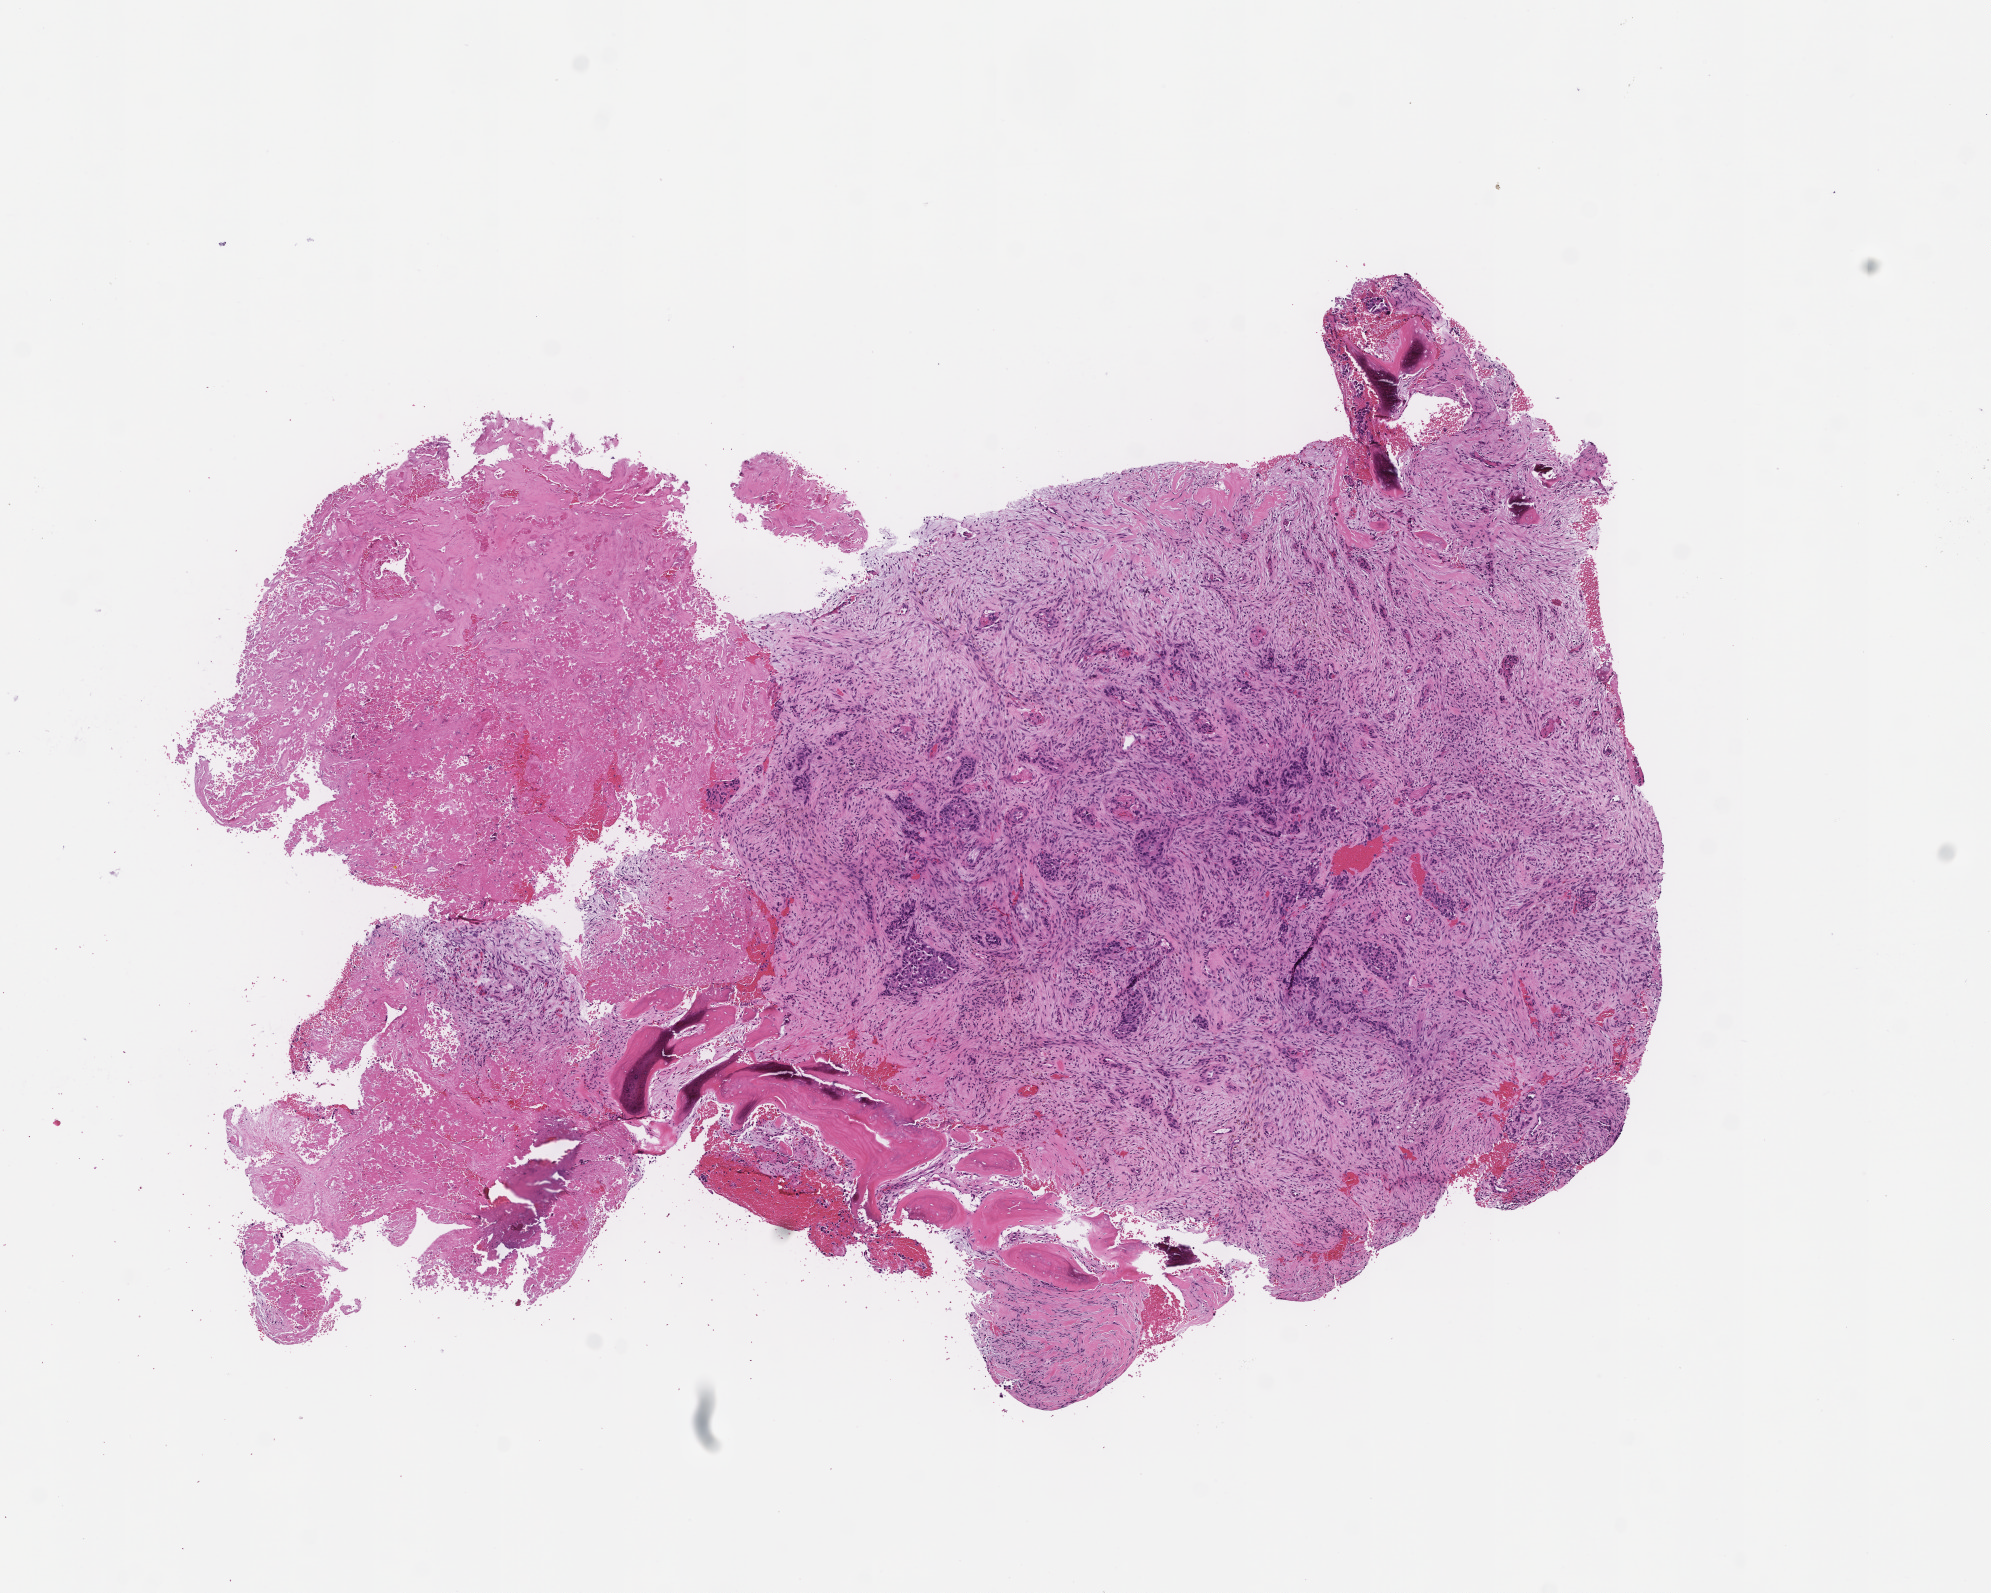
Hematoxylin and eosin (H&E) whole-slide image, low-resolution overview of the scanned area, about 8.0 x 6.4 mm; formalin-fixed paraffin-embedded section; specimen time point: collected at baseline (before treatment). Patient: male.
This section: metastasis (sampled organ not recorded). Patient diagnosis (primary): Invasive Breast Carcinoma.